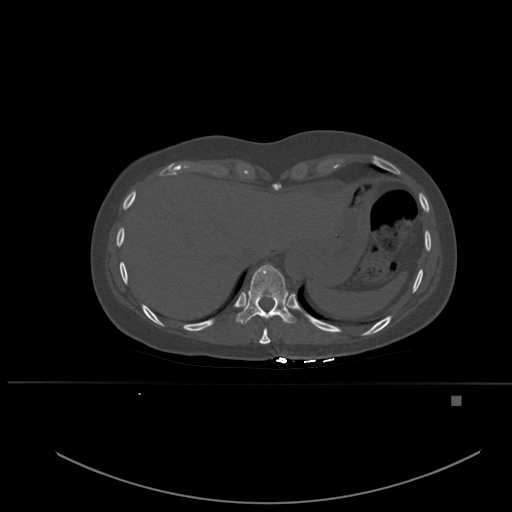
CT including the spine, one axial slice. Position 293 of 651 along the scan axis. Bone window (W 1800 / L 400 HU). 512 × 512 image matrix, field of view 443 × 443 mm. Female patient, age 49 years. Case-level facts recorded for this patient, not image findings: primary cancer: breast; vertebrae with lytic lesions (as recorded): L3, T12, L4.
Structures marked on this image (semi-automatically segmented with operator editing):
- T10 vertebra: bounding box (x1, y1, x2, y2) in pixels: (236, 264, 296, 325)
- T9 vertebra: (259, 317, 271, 344)